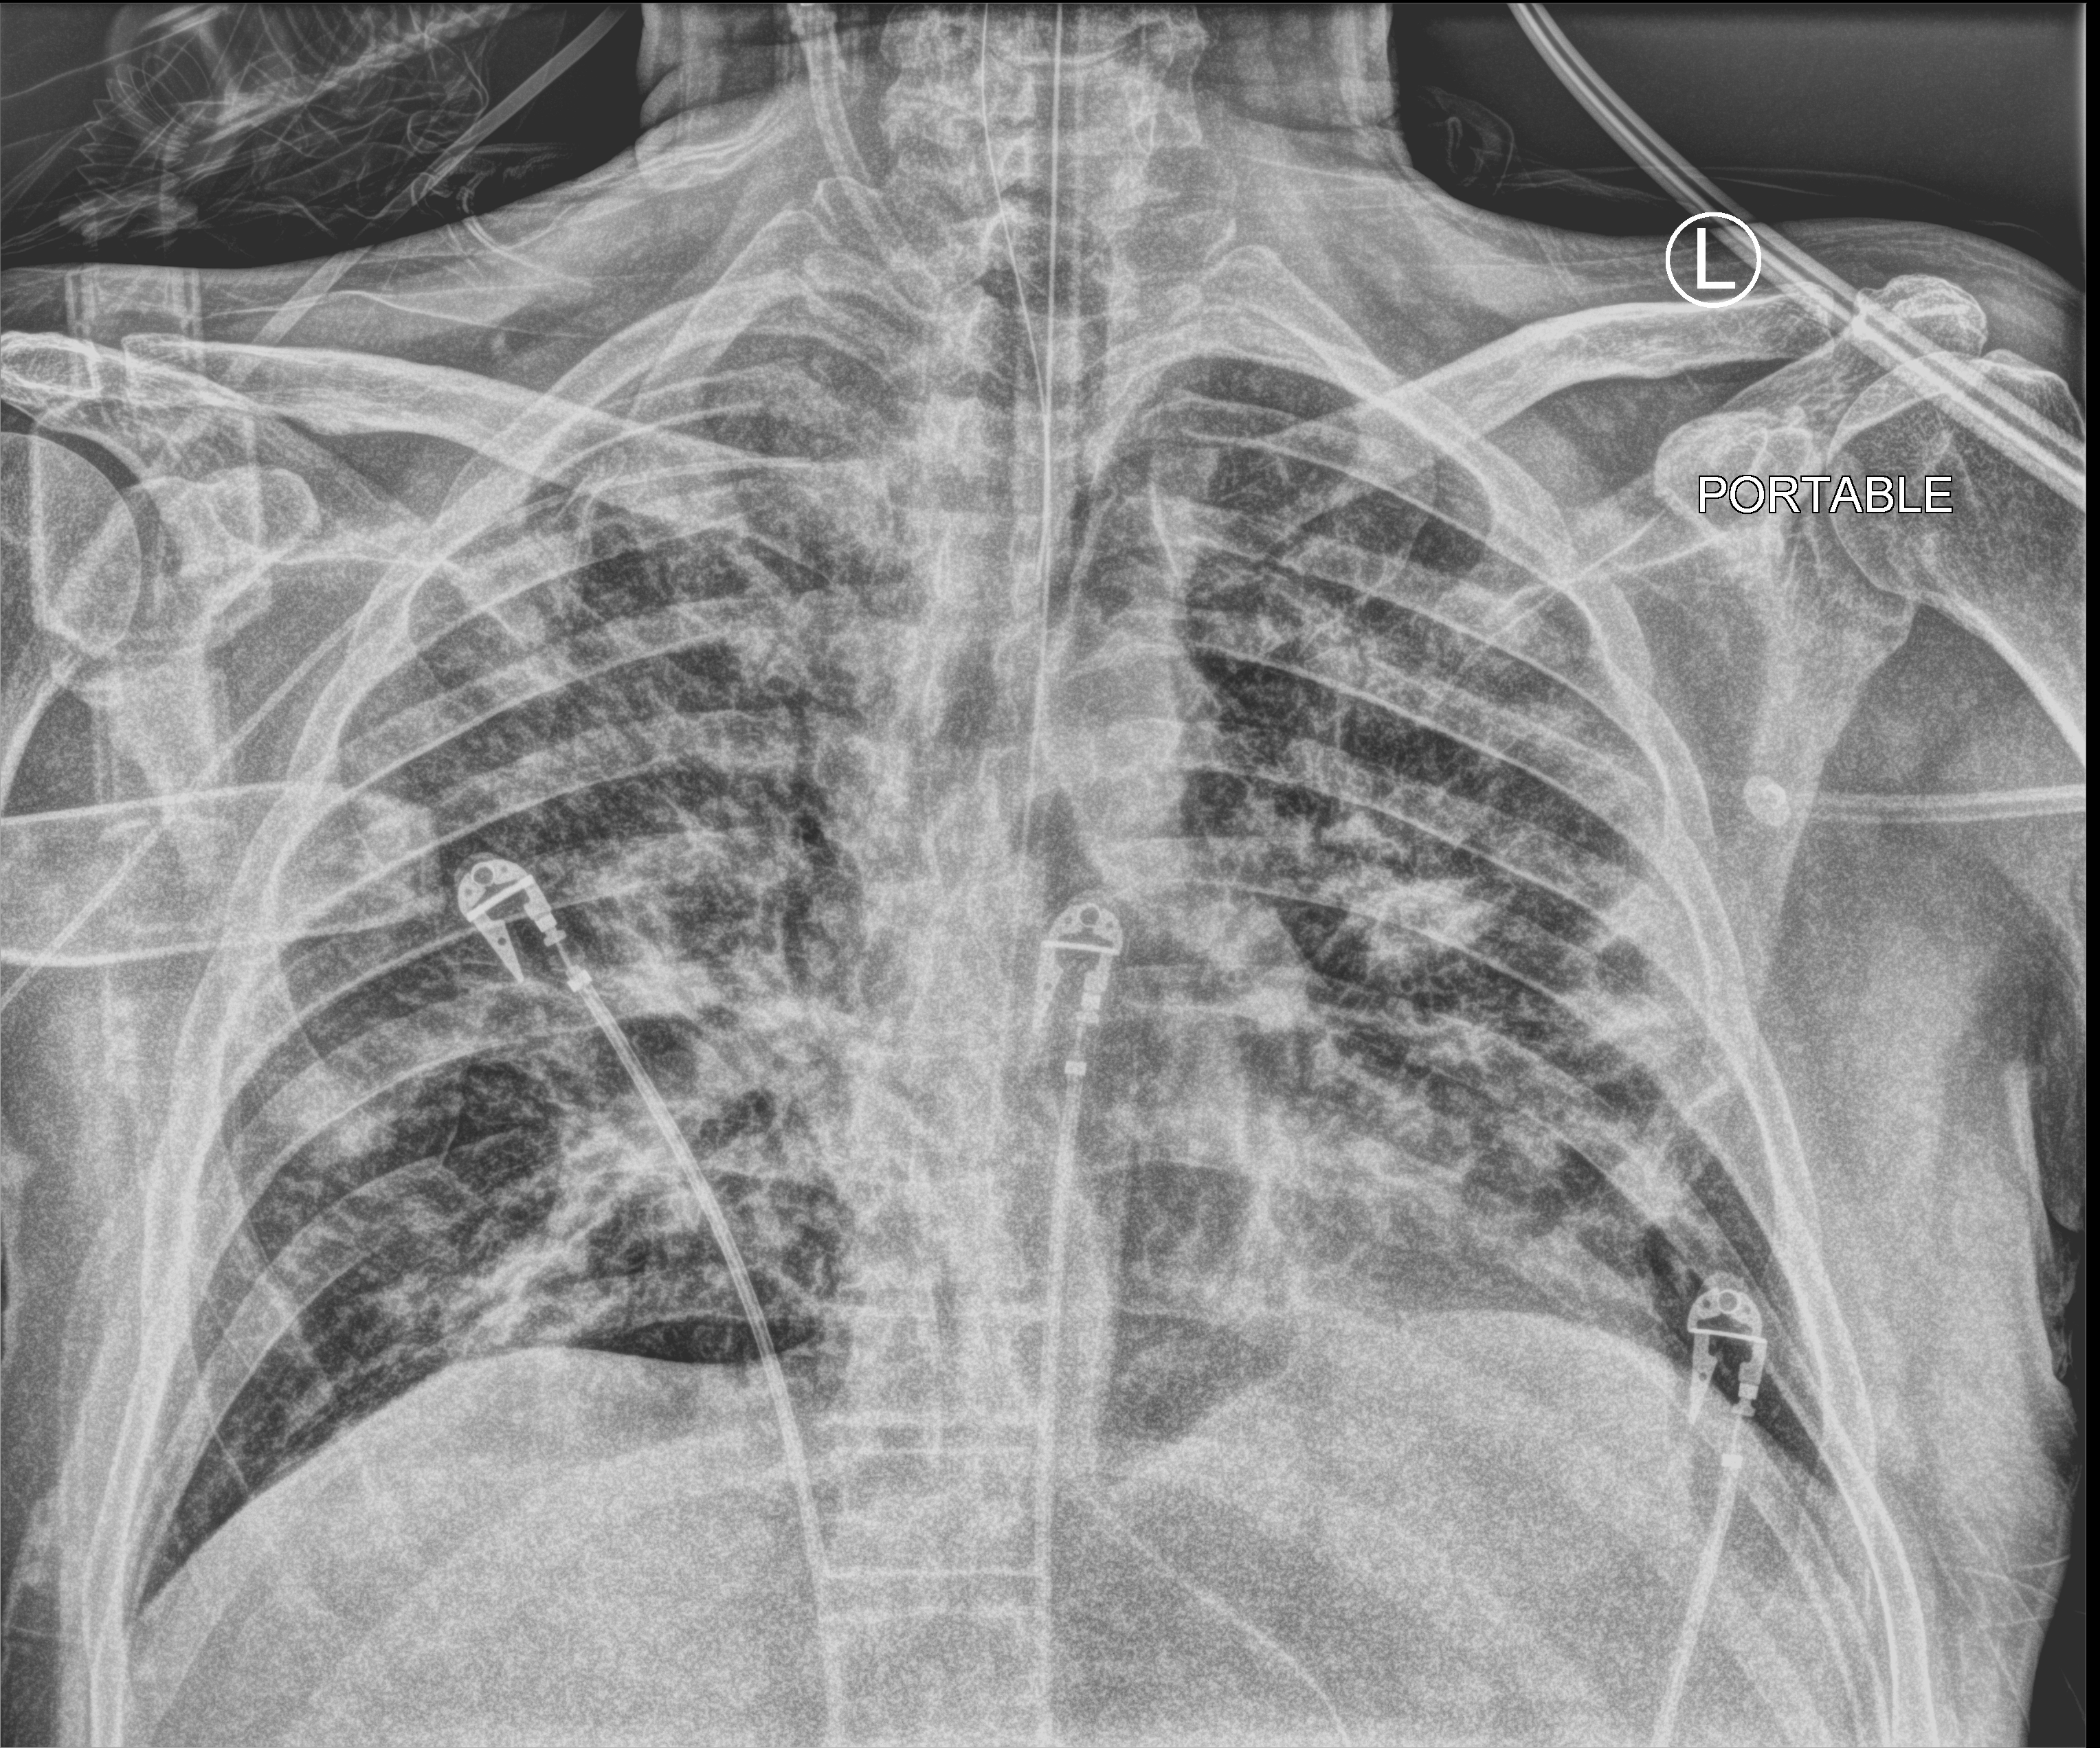
Chest X-ray (portable). Male patient hospitalised with COVID-19, age 60–74 years.
Hospital-stay facts (about this admission, not read from this image; timing relative to this image not recorded):
- admitted to intensive care during this hospital stay: yes